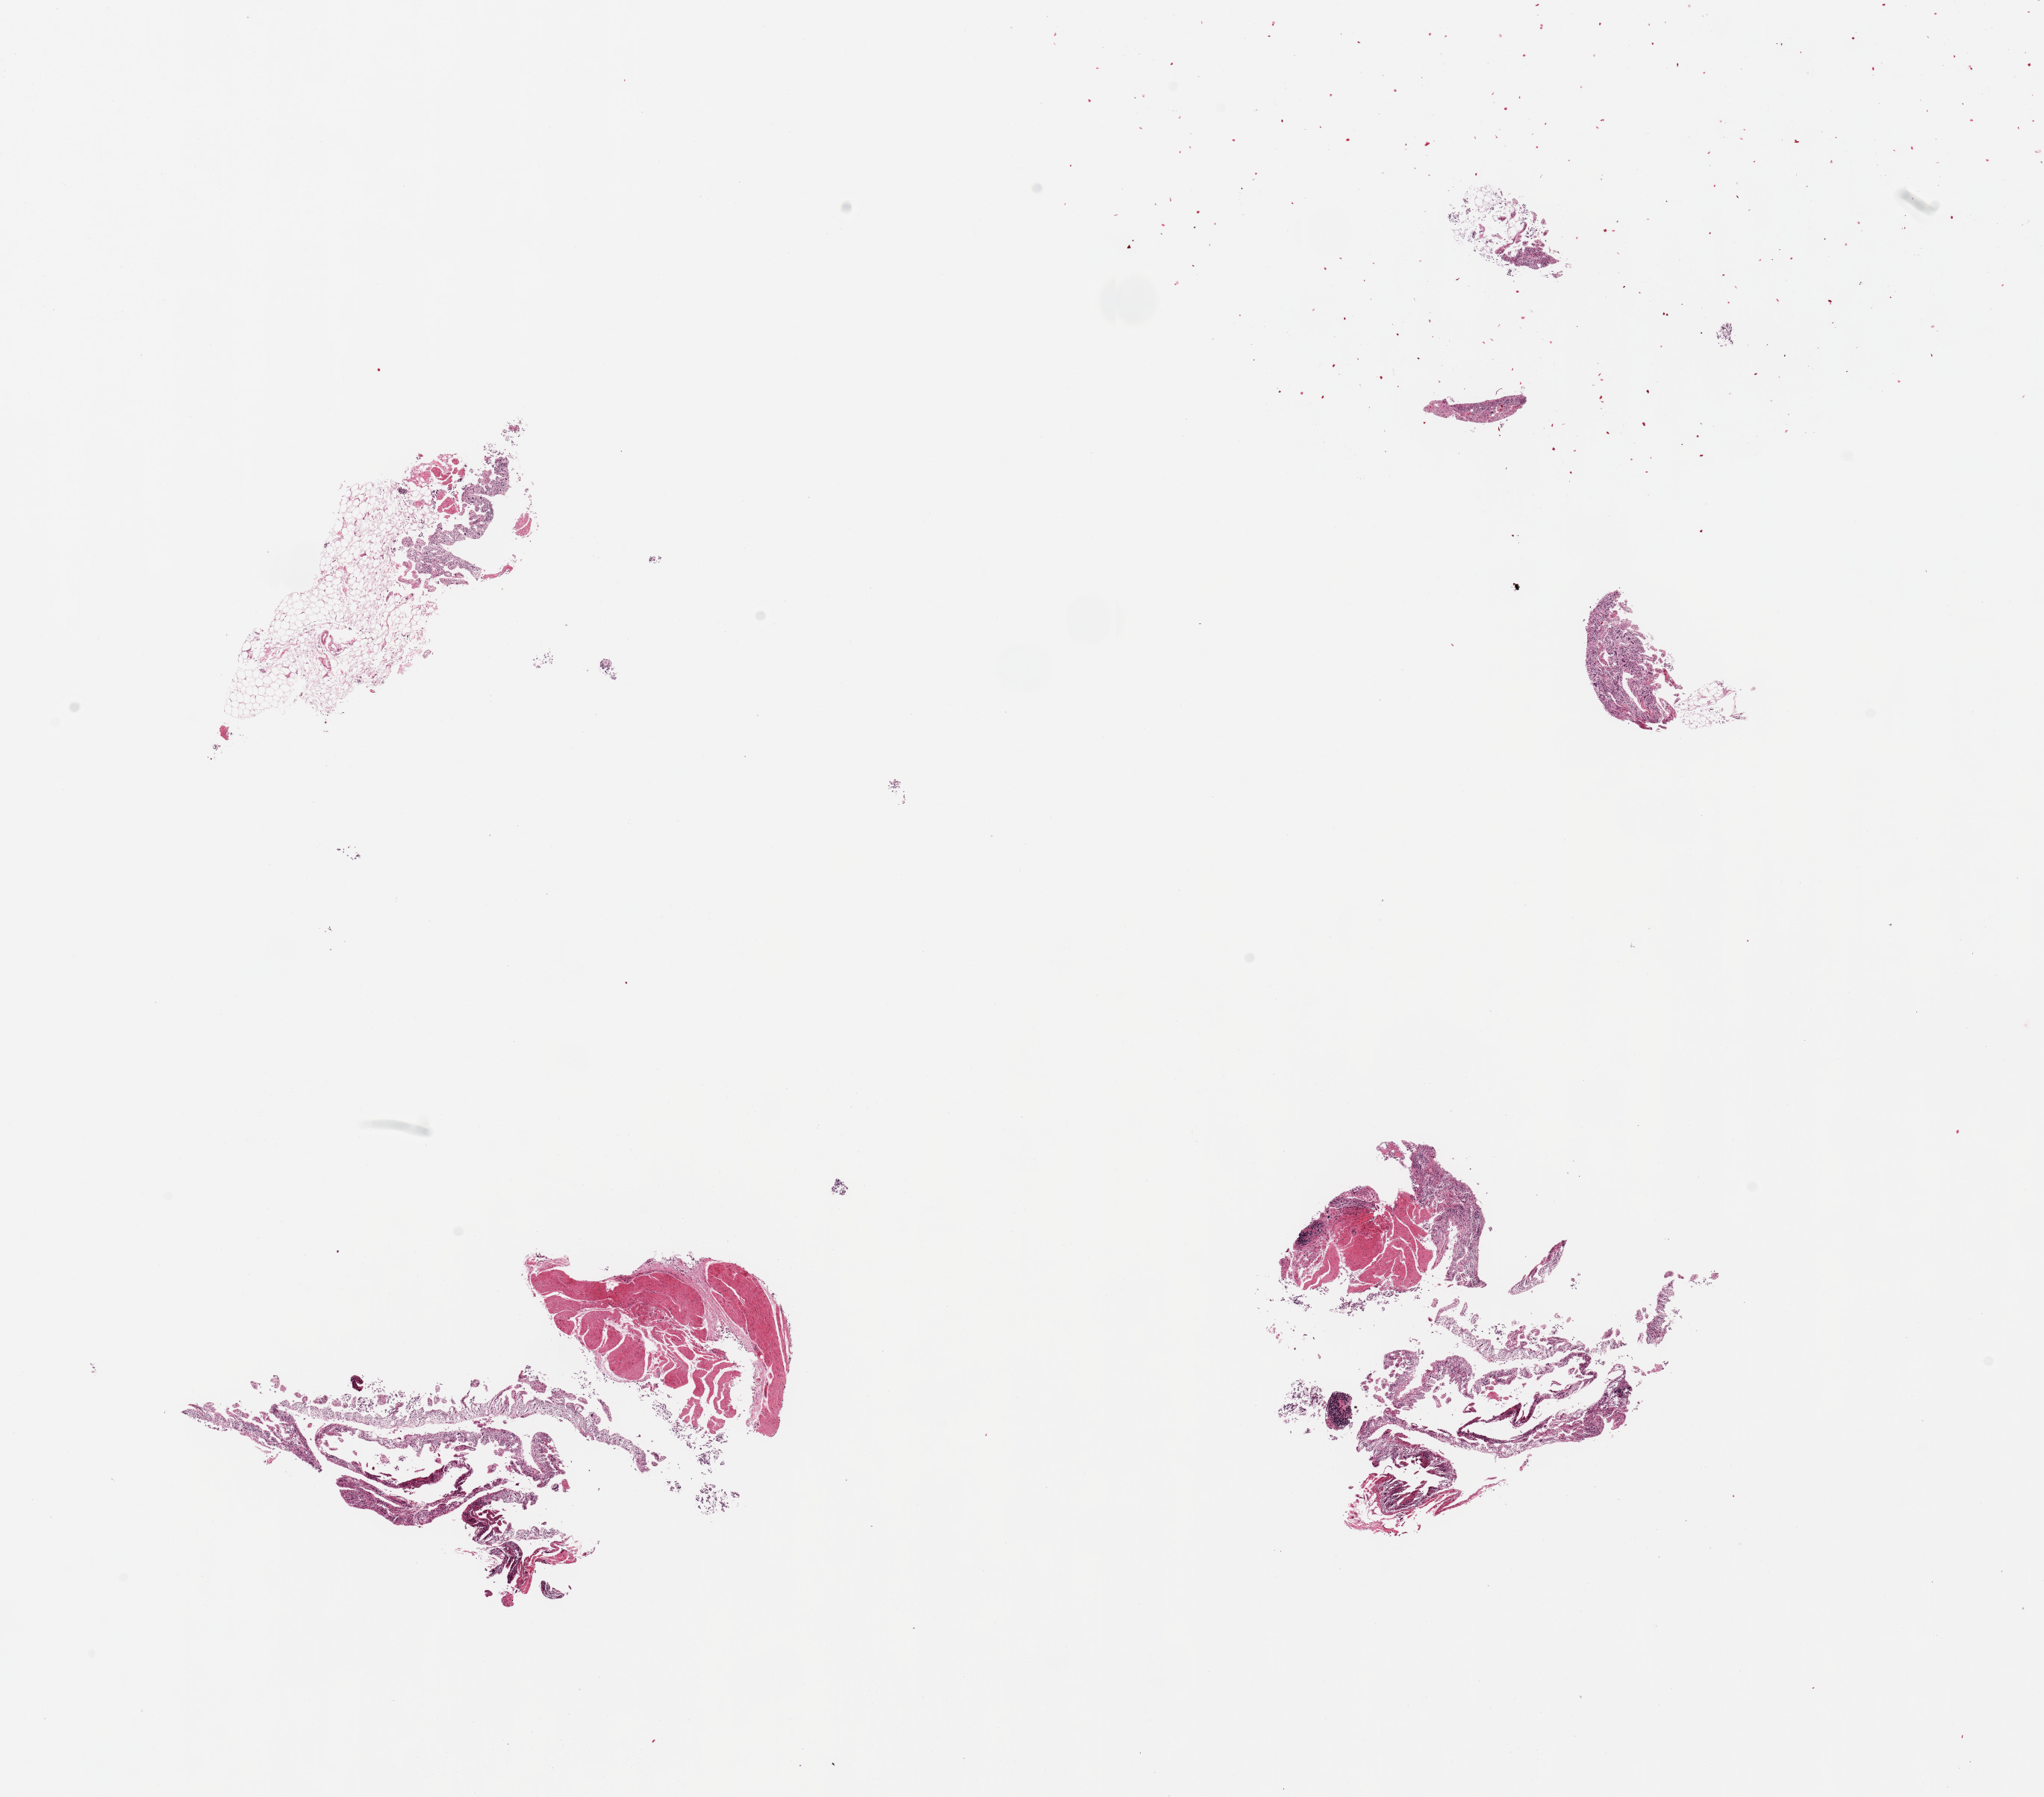
Digitized hematoxylin and eosin (H&E)-stained section, shown as a low-resolution overview of the whole scanned area (about 21.7 x 19.0 mm, acquisition: 20x scan). PAXgene-fixed, paraffin-embedded tissue. Section of ileum (target tissue). Donor tissue sample. Male donor.
Pathologist's review note for this sample: 4 pieces; fragments of autolyzed mucosa, muscularis, and fat; no lymphoid tissue.